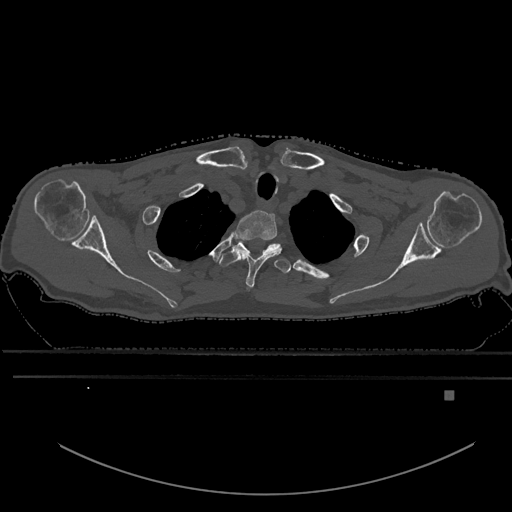
CT including the spine, one axial slice. Slice 517 of 969 in the series (ordered by position). Bone window (W 1800 / L 400 HU). 512 × 512 image matrix, field of view 456 × 456 mm. Patient: male, 82 years. Case-level facts recorded for this patient, not image findings: primary cancer: prostate; vertebrae with lytic lesions (as recorded): T11, T9, T8, T2.
Structures marked on this image (semi-automatically segmented with operator editing):
- T1 vertebra: bounding box [x1, y1, x2, y2] px = [234, 210, 279, 292]
- T2 vertebra: [219, 239, 279, 267]